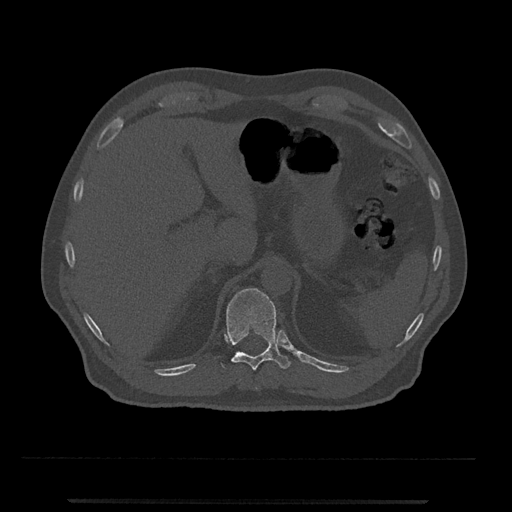
CT including the spine, one axial slice. Reconstruction kernel Br40s/3. 120 kVp. Bone window (W 1800 / L 400 HU). 512 × 512 image matrix, field of view 419 × 419 mm. Male patient, age 63 years. Case-level facts recorded for this patient, not image findings: primary cancer: prostate.
Outlined on this slice (semi-automatic segmentation, software-assisted and operator-edited):
- T11 vertebra: bounding box (x1, y1, x2, y2) in pixels: (222, 288, 291, 371)